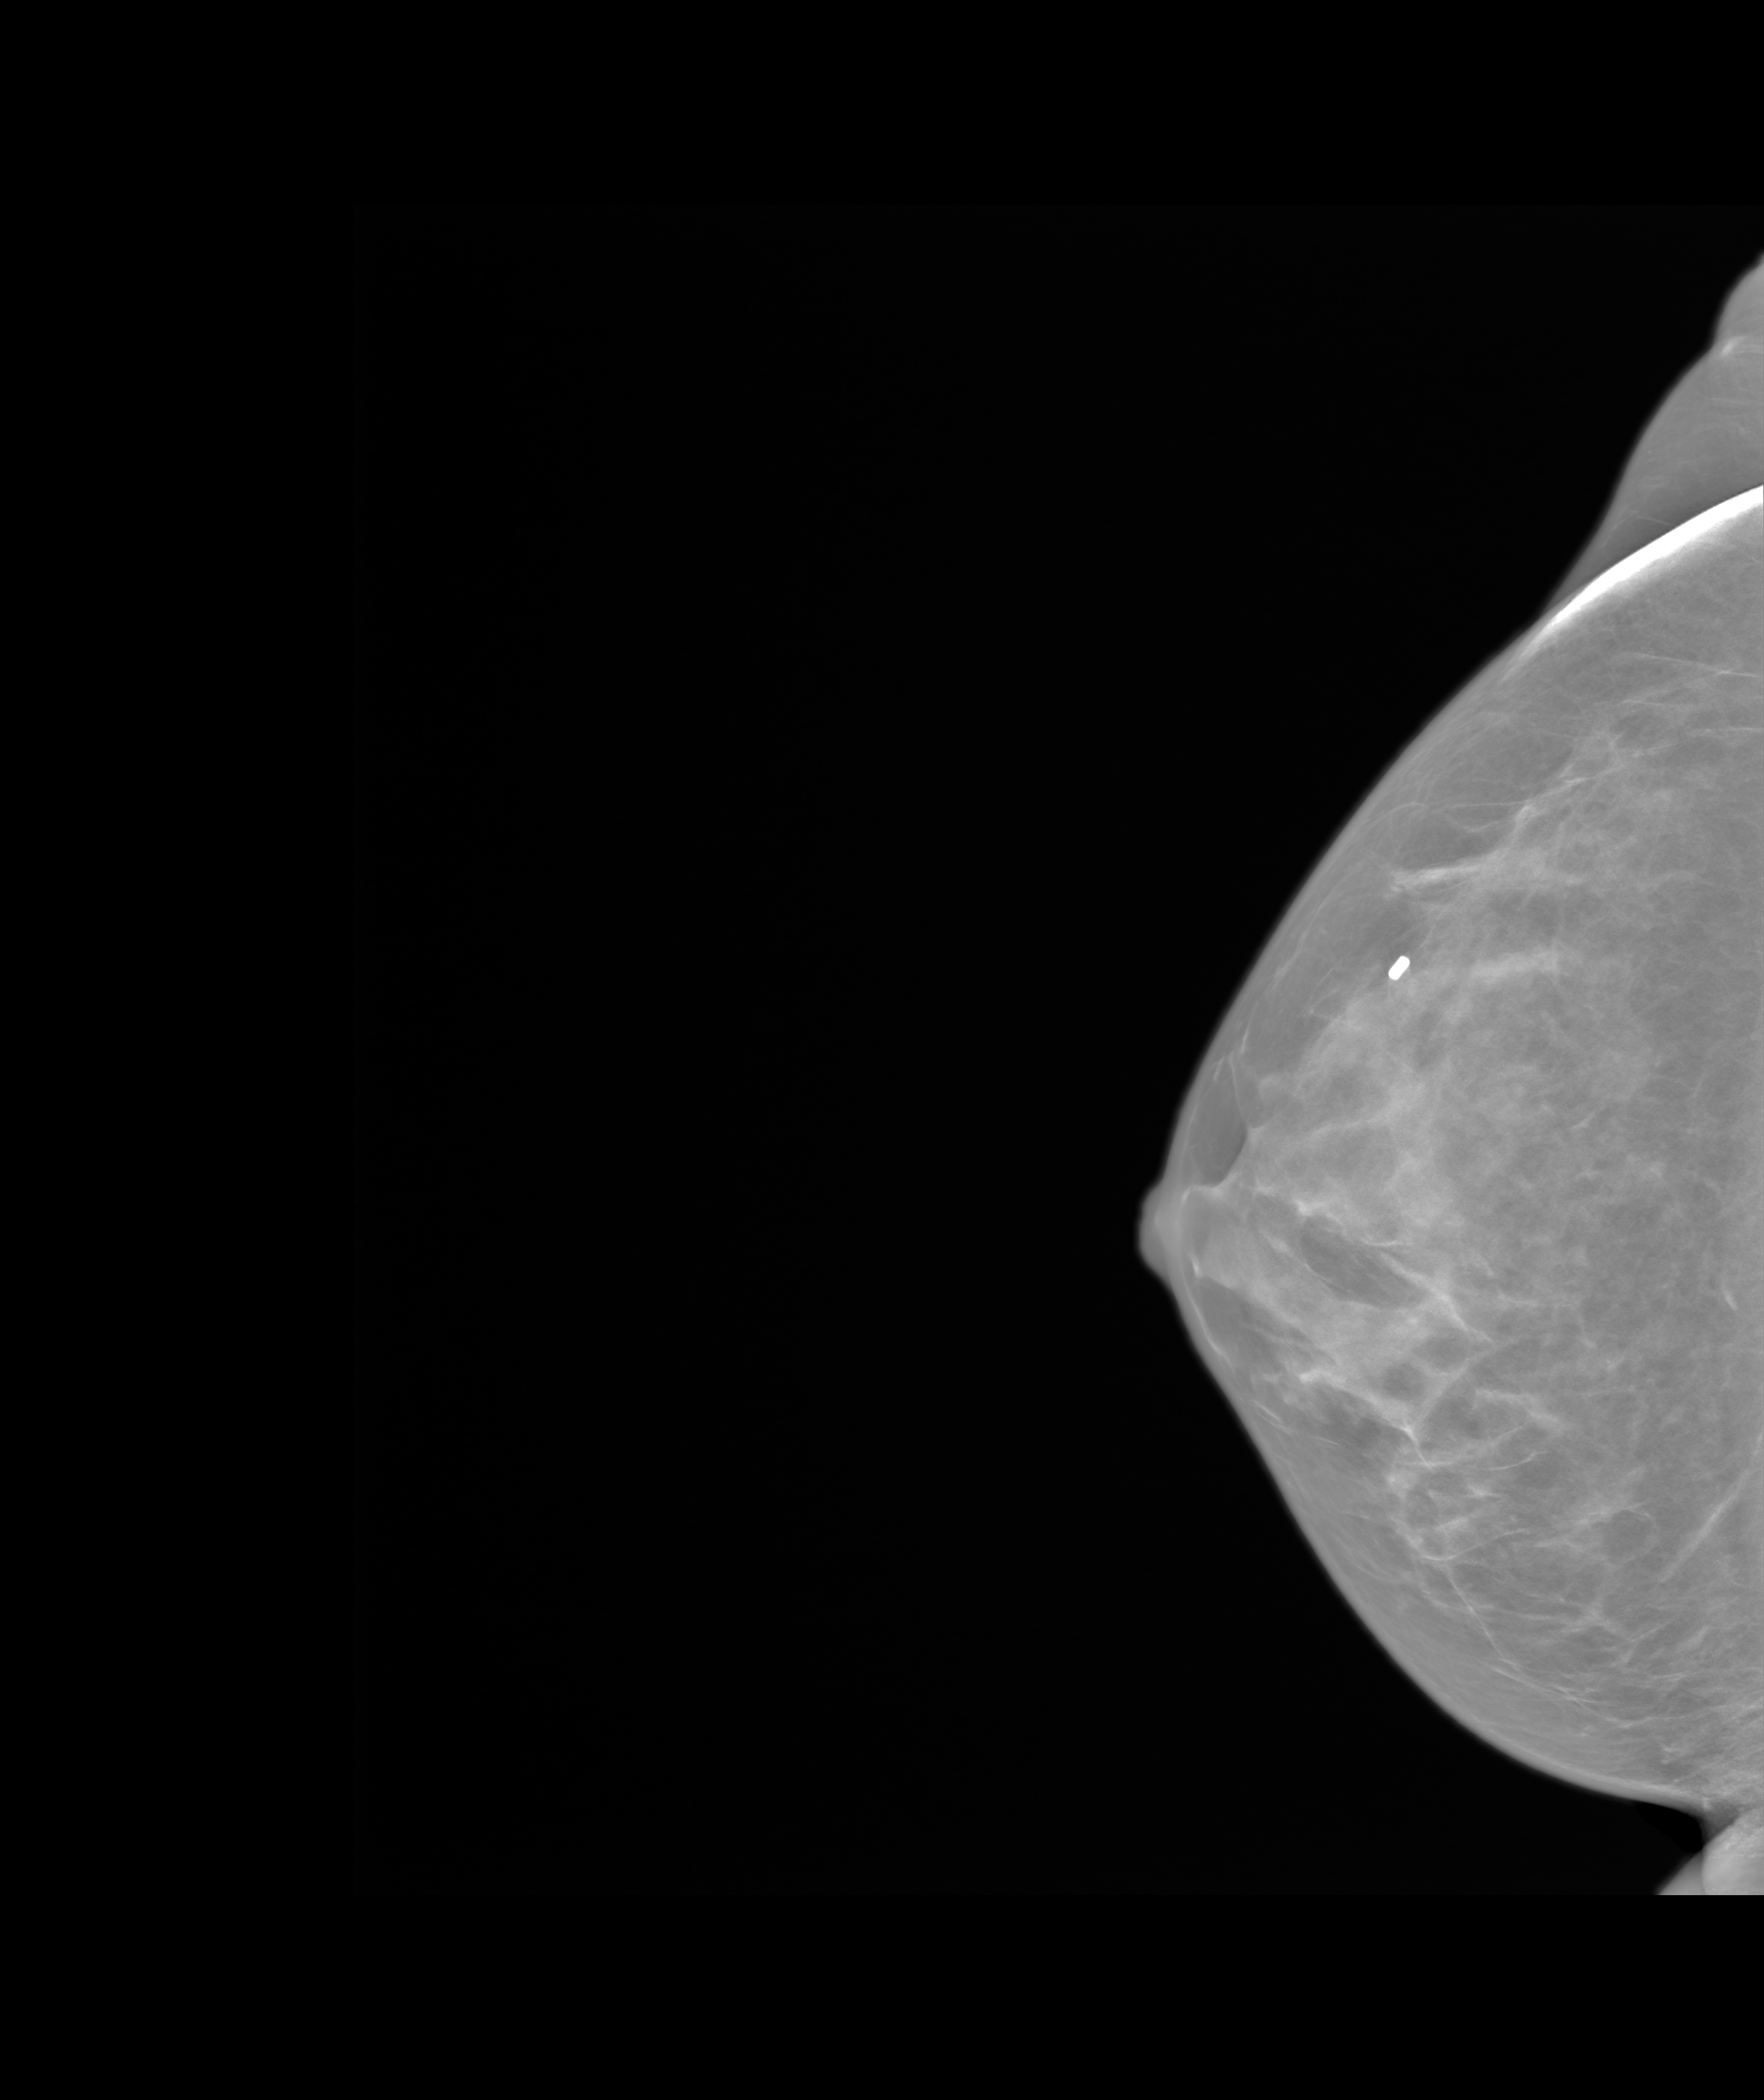
Screening examination. Patient aged 43 years (female).
Image type: synthesized 2-D view from tomosynthesis. Breast: right. Projection: CC view.